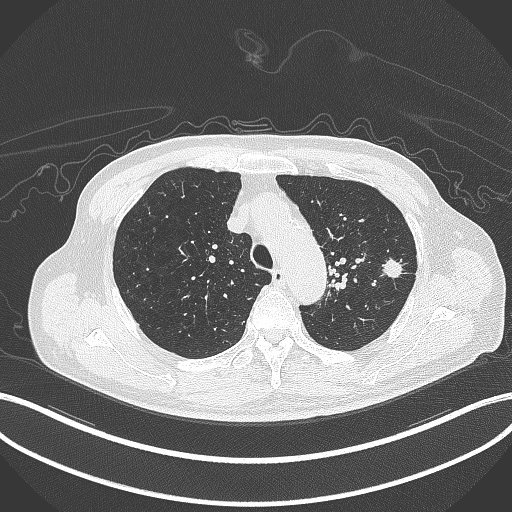
Chest CT, one axial slice. Position 337 of 417 along the scan axis. Reconstruction kernel B70f. Lung window (W 1500 / L -600 HU). 1 mm slice thickness. 512 × 512 image matrix, field of view 400 × 400 mm. Patient: male, 77 years. From the clinical record (not read from this slice): clinical TNM (as recorded): T3 N1 M0.
Annotated regions visible in this slice (bounding box drawn by a radiologist):
- lung tumour (recorded histology: adenocarcinoma): bounding box [x1, y1, x2, y2] px = [381, 253, 405, 282]